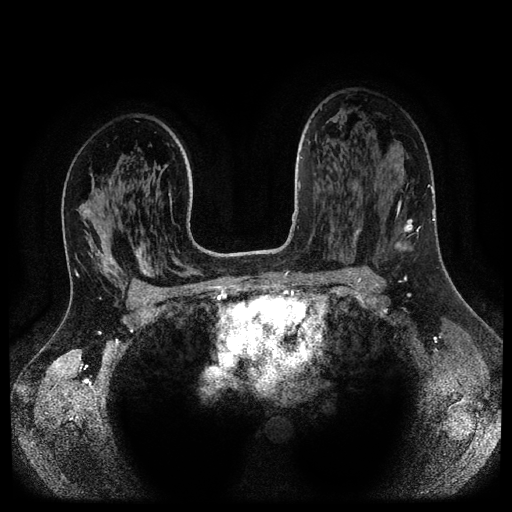
Breast MRI (dynamic contrast-enhanced, multi-phase), one axial slice. Slice 69 of 116 in the series (ordered by position). Dynamic contrast-enhanced series, time point 2 of 5 at this slice position (early post-contrast). 1.5 T. TE 2.6 ms, TR 5.3 ms. 2.1 mm slice thickness. 512 × 512 image matrix, field of view 360 × 360 mm. Patient: female, 37 years.
Annotated regions visible in this slice (semi-automatic segmentation, software-assisted and operator-edited):
- breast lesion (labelled 'tumour' in the annotation; benign lesions carry a separate 'benign' label): bounding box [x1, y1, x2, y2] px = [394, 219, 415, 251]